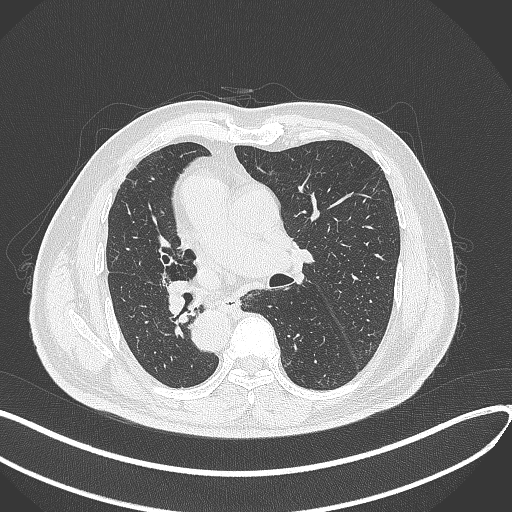
Chest CT, one axial slice. Slice 153 of 300 in the series (ordered by position). Reconstruction kernel B70f. Lung window (W 1500 / L -600 HU). 512 × 512 image matrix. Patient: male, 67 years. Case-level facts recorded for this patient, not image findings: clinical TNM (as recorded): T2a N0 M0.
Structures marked on this image (bounding box drawn by a radiologist):
- lung tumour (recorded histology: squamous cell carcinoma): bounding box <165,279,187,318> (left, top, right, bottom; pixels)